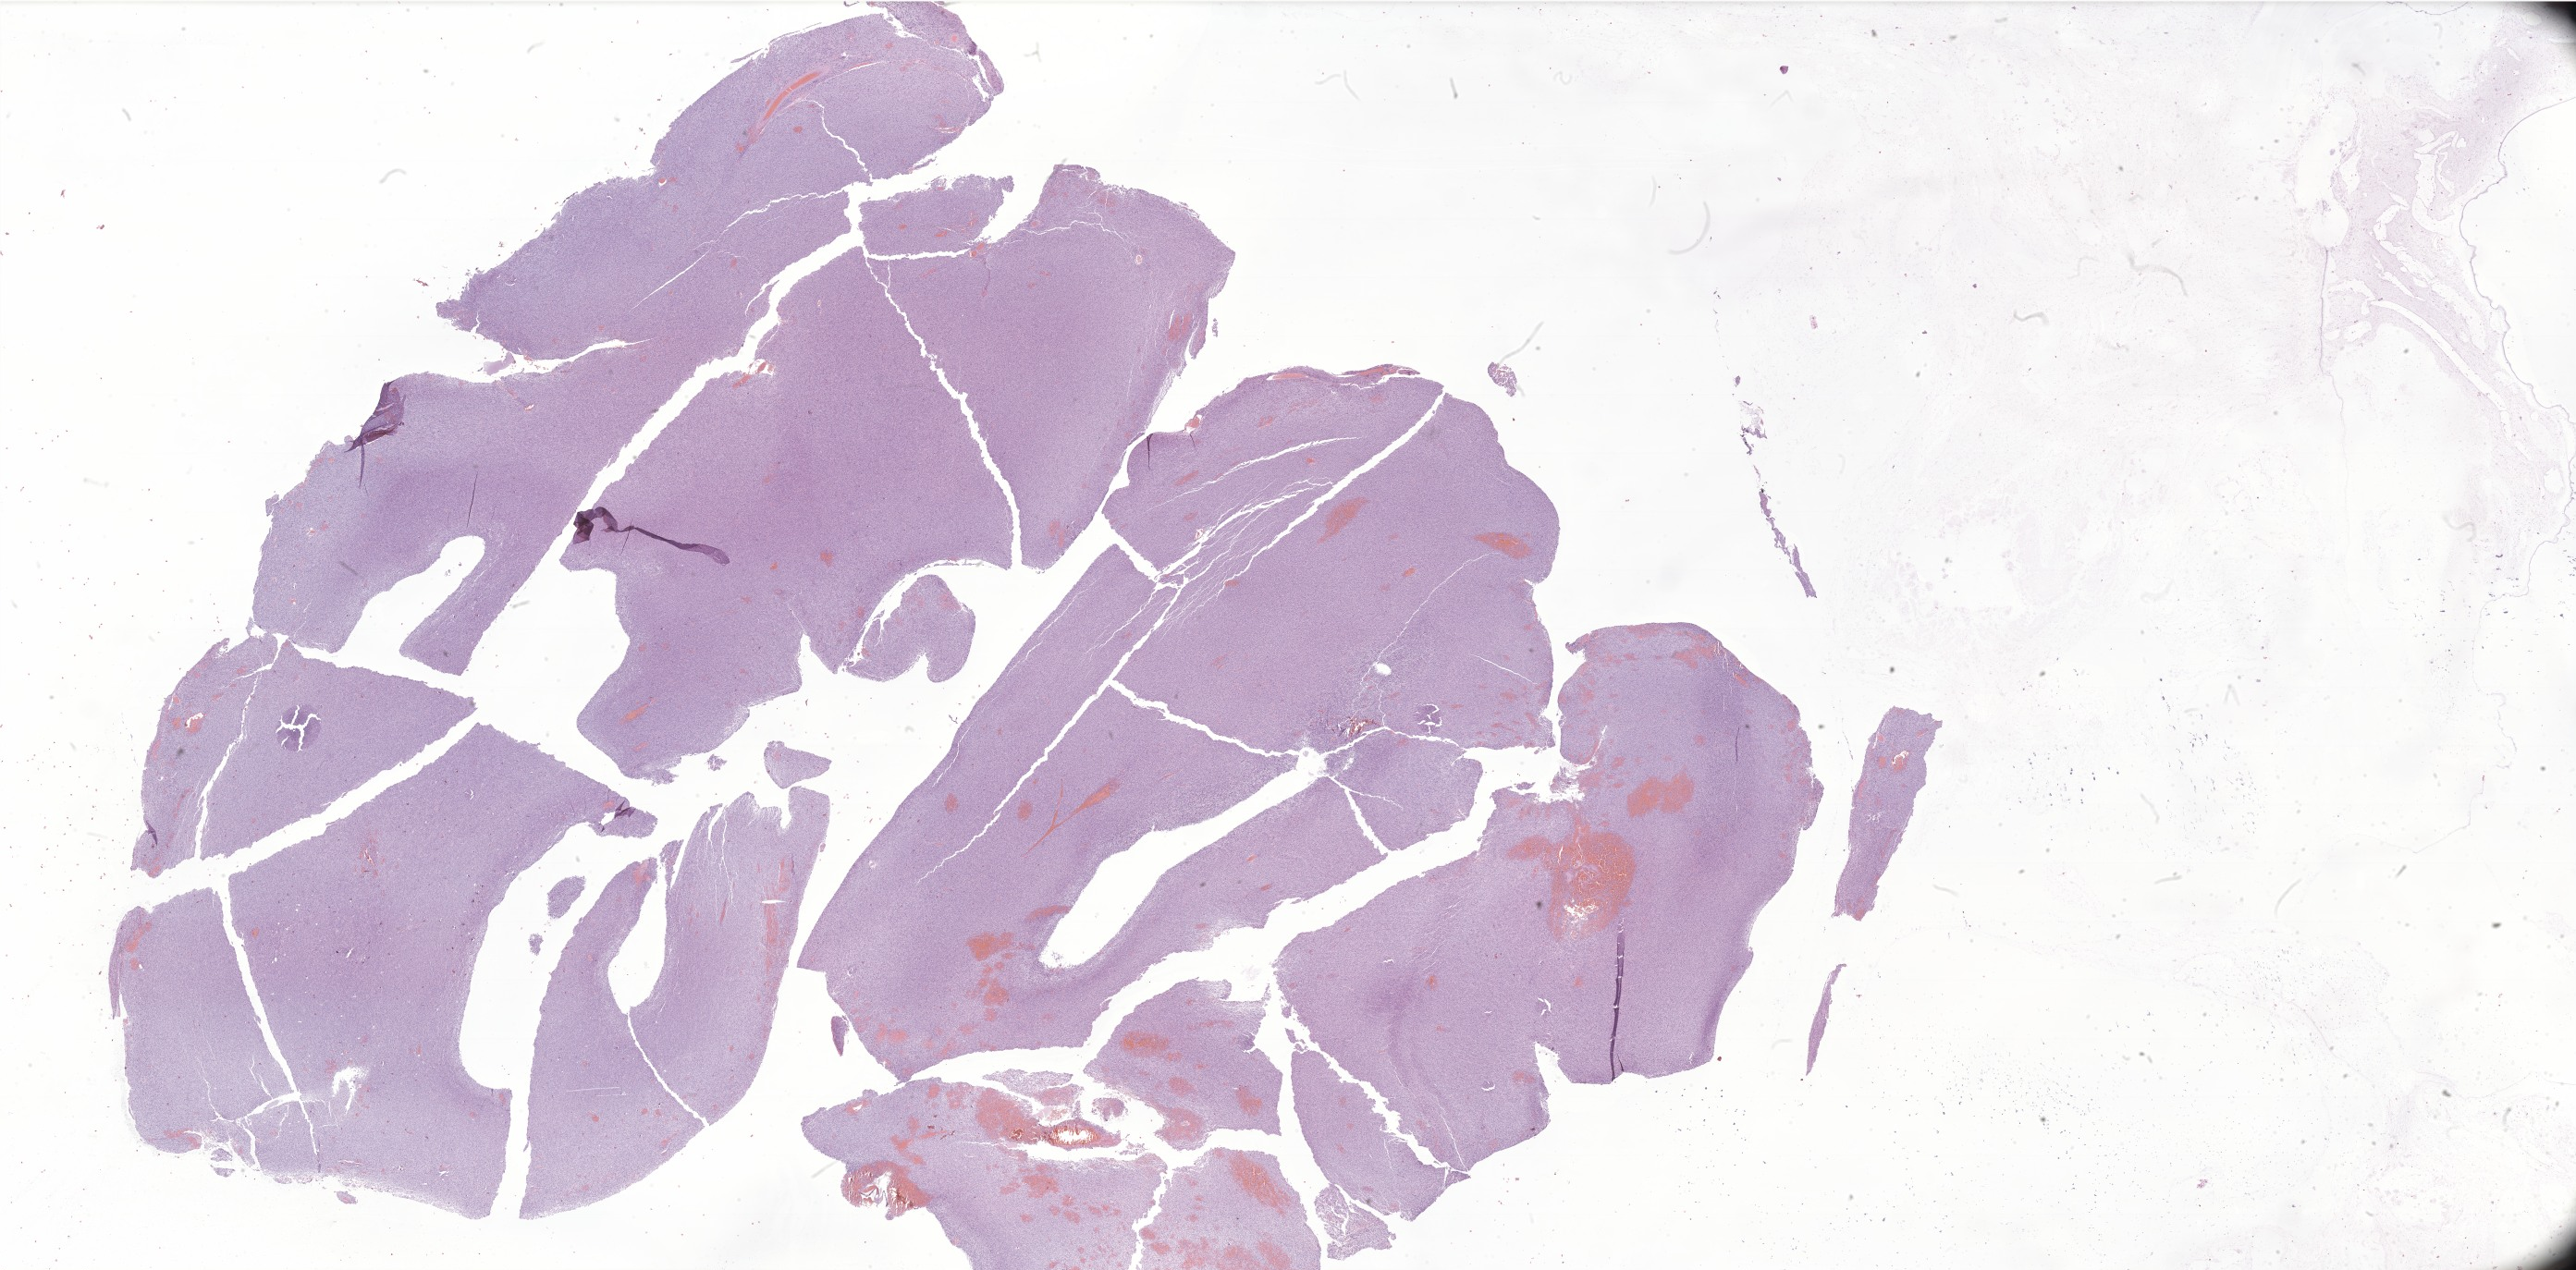
Hematoxylin and eosin (H&E) whole-slide image of tumor tissue from the temporal lobe, a low-resolution overview of the entire scanned area, about 47.0 x 23.2 mm, formalin-fixed, paraffin-embedded (FFPE) tissue. Male patient, age 180 months (15 years).
Diagnosis (ICD-O-3 morphology term): Epithelial tumor, benign.